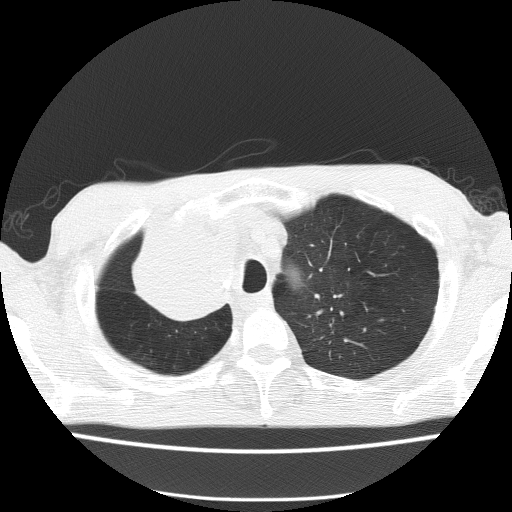
Low-dose screening chest CT, one axial slice. Slice 121 of 150 in the series (ordered by position). 120 kVp. Lung window (W 1500 / L -600 HU). 512 × 512 image matrix, field of view 336 × 336 mm.
Outlined on this slice (expert manual segmentation):
- lesion 1 (tumor, hilum of right lung): box from (x=134, y=220) to (x=225, y=320) px